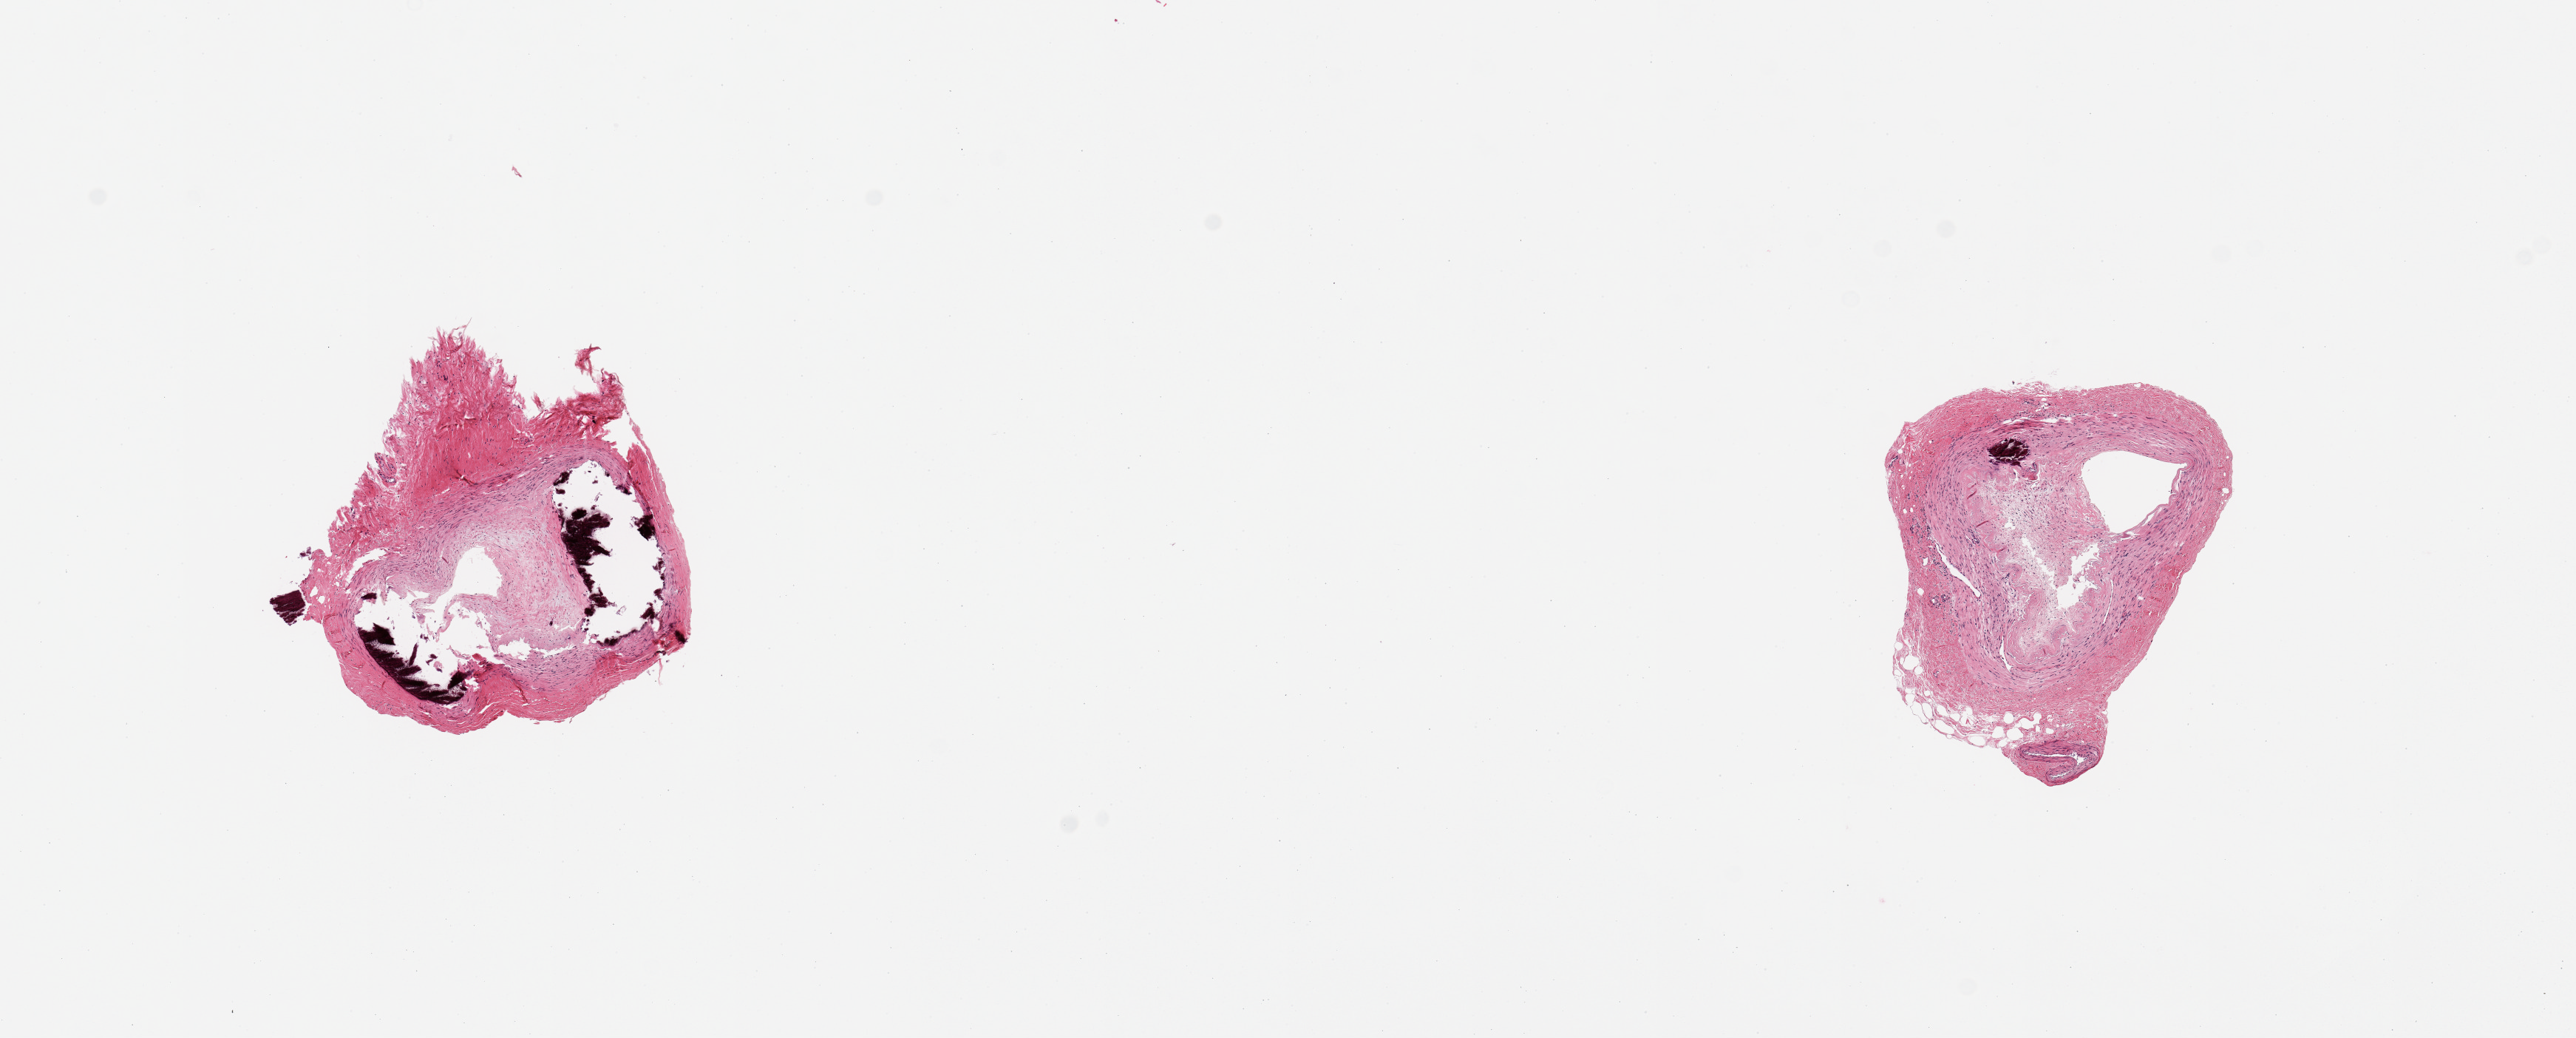
Digitized haematoxylin and eosin-stained section, brightfield — whole scanned area (about 13.8 x 5.6 mm) shown as a low-resolution overview. PAXgene-fixed, paraffin-embedded tissue. Sampled site (target tissue): tibial artery. Donor tissue sample. Female donor.
Pathologist's review note for this sample: 2 pieces; medial calcification and atheromatous change, markedly compromising lumen.